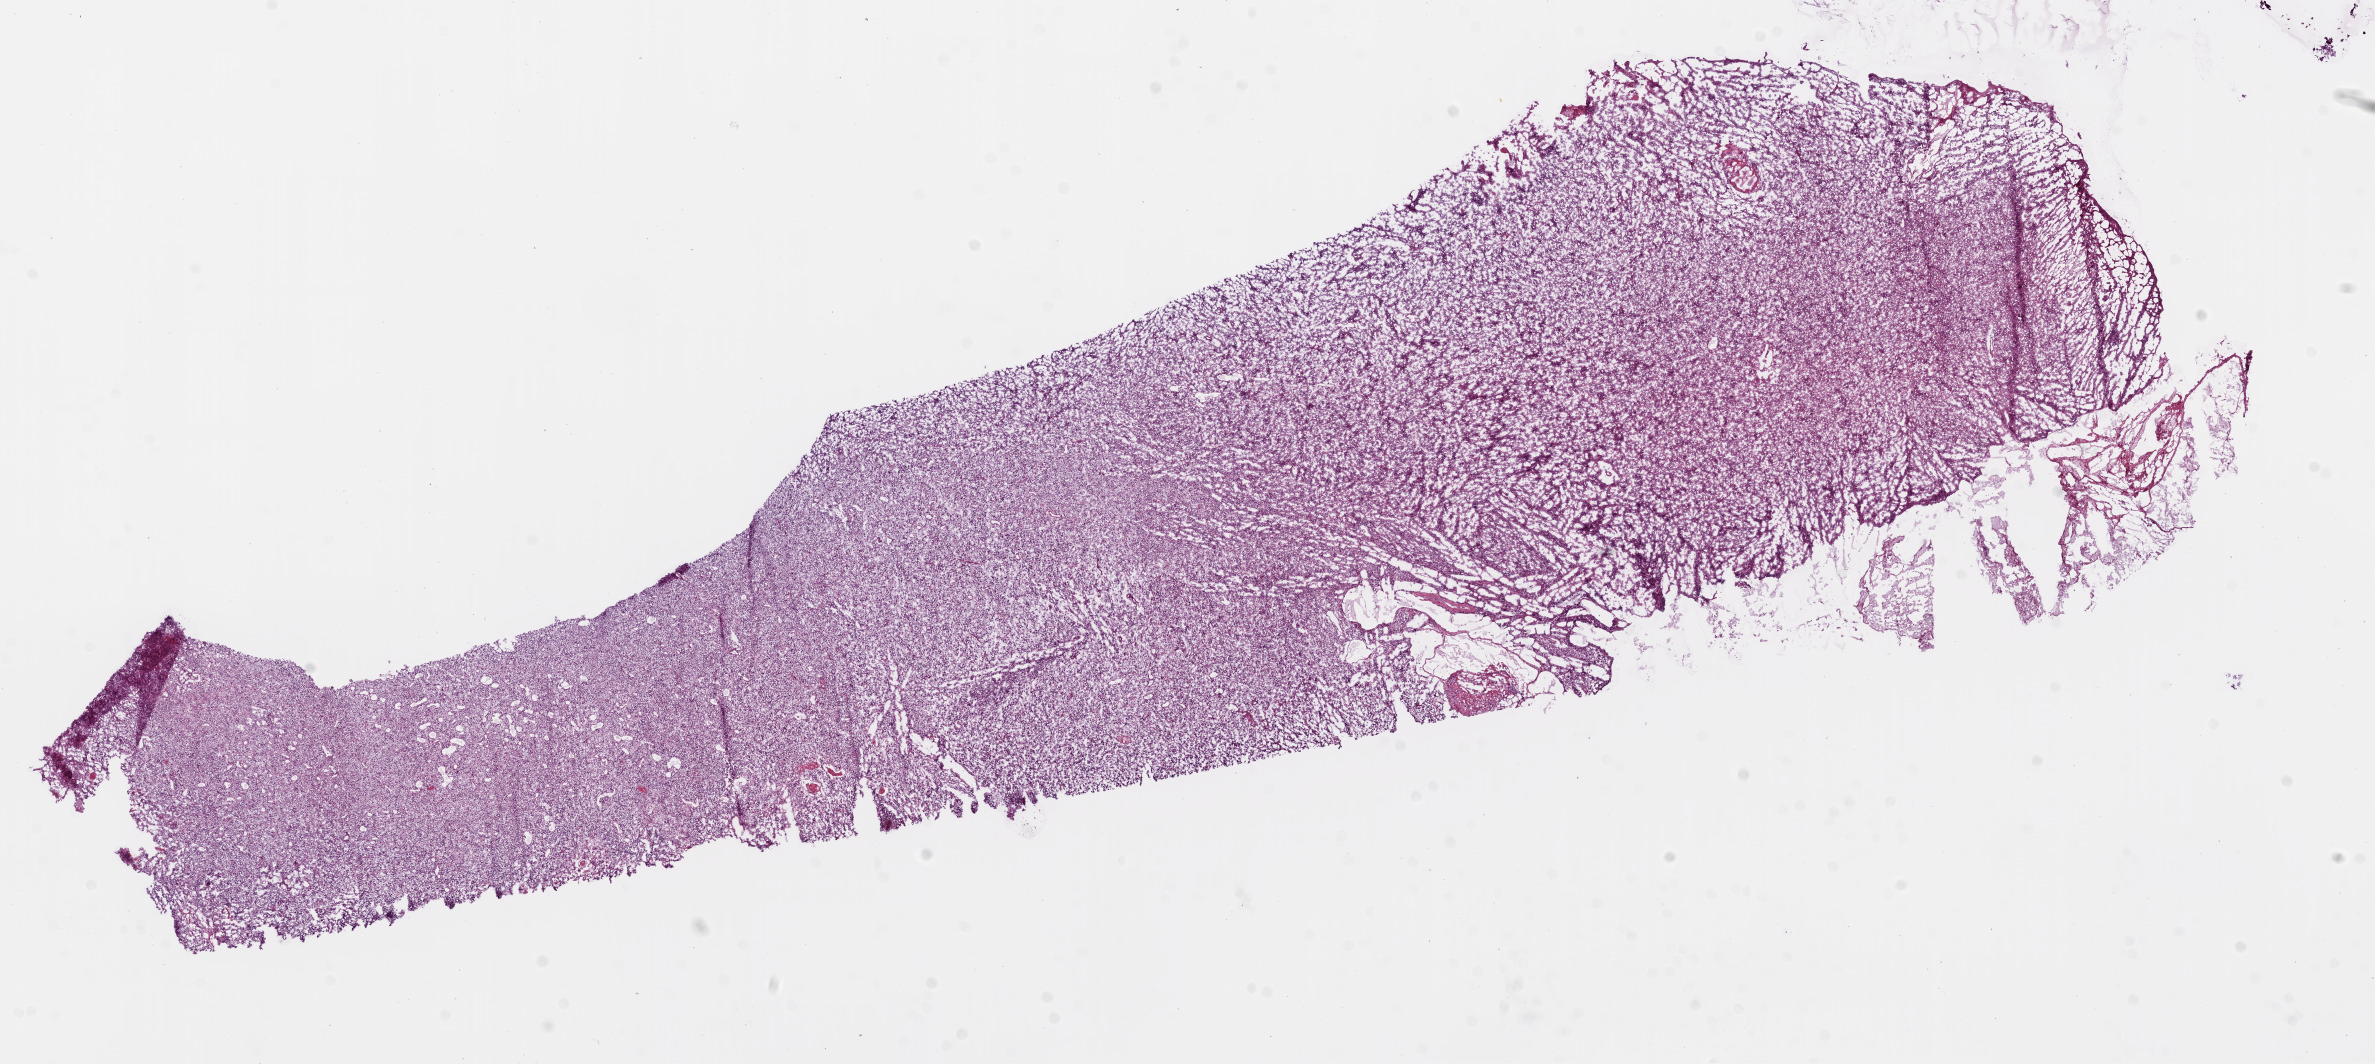
H&E whole-slide image, shown as a low-resolution overview of the whole scanned area (about 19.1 x 8.5 mm). Frozen section from the bottom of the tissue portion. Sample: primary tumour, brain. Female, age 50 years at initial diagnosis. Slide review estimates, as recorded: tumour cells 100%, tumour nuclei 85%, normal cells 0%, stromal cells 0%, necrosis 0%.
Diagnosis: Glioblastoma.